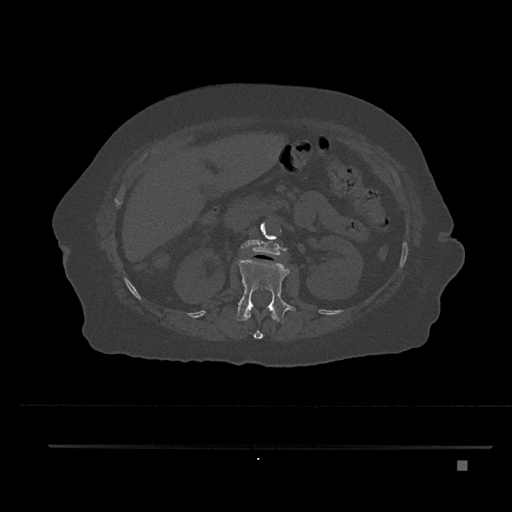
CT including the spine, one axial slice; reconstruction kernel Br40s/3; 120 kVp; bone window (W 1800 / L 400 HU); 0.5 mm slice thickness; 512 × 512 image matrix. Patient: female, 76 years. From the clinical record (not read from this slice): primary cancer: lung; vertebrae with lytic lesions (as recorded): T11, L3.
Annotated regions visible in this slice (semi-automatic segmentation, software-assisted and operator-edited):
- L1 vertebra: box from (x=236, y=258) to (x=296, y=324) px
- L2 vertebra: (x=241, y=239)–(x=285, y=255)
- T12 vertebra: (x=244, y=309)–(x=277, y=339)